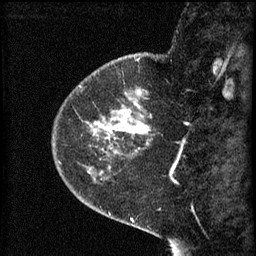
Breast MRI (dynamic contrast-enhanced), one sagittal slice. Position 16 of 60 along the scan axis. 3 images stored at this slice position (order not interpretable as contrast timing). 1.5 T. TE 4.2 ms, TR 8.2 ms. 2 mm slice thickness. 256 × 256 image matrix. Female patient, age 44 years.
Outlined on this slice (semi-automatically segmented with operator editing):
- analysis volume of interest (the breast-tissue region the enhancement analysis was run in; not a lesion): box from (x=73, y=82) to (x=152, y=165) px
- tumour enhancement mask (voxels above the 70 % enhancement threshold inside the analysis volume of interest): (x=88, y=90)–(x=152, y=153)